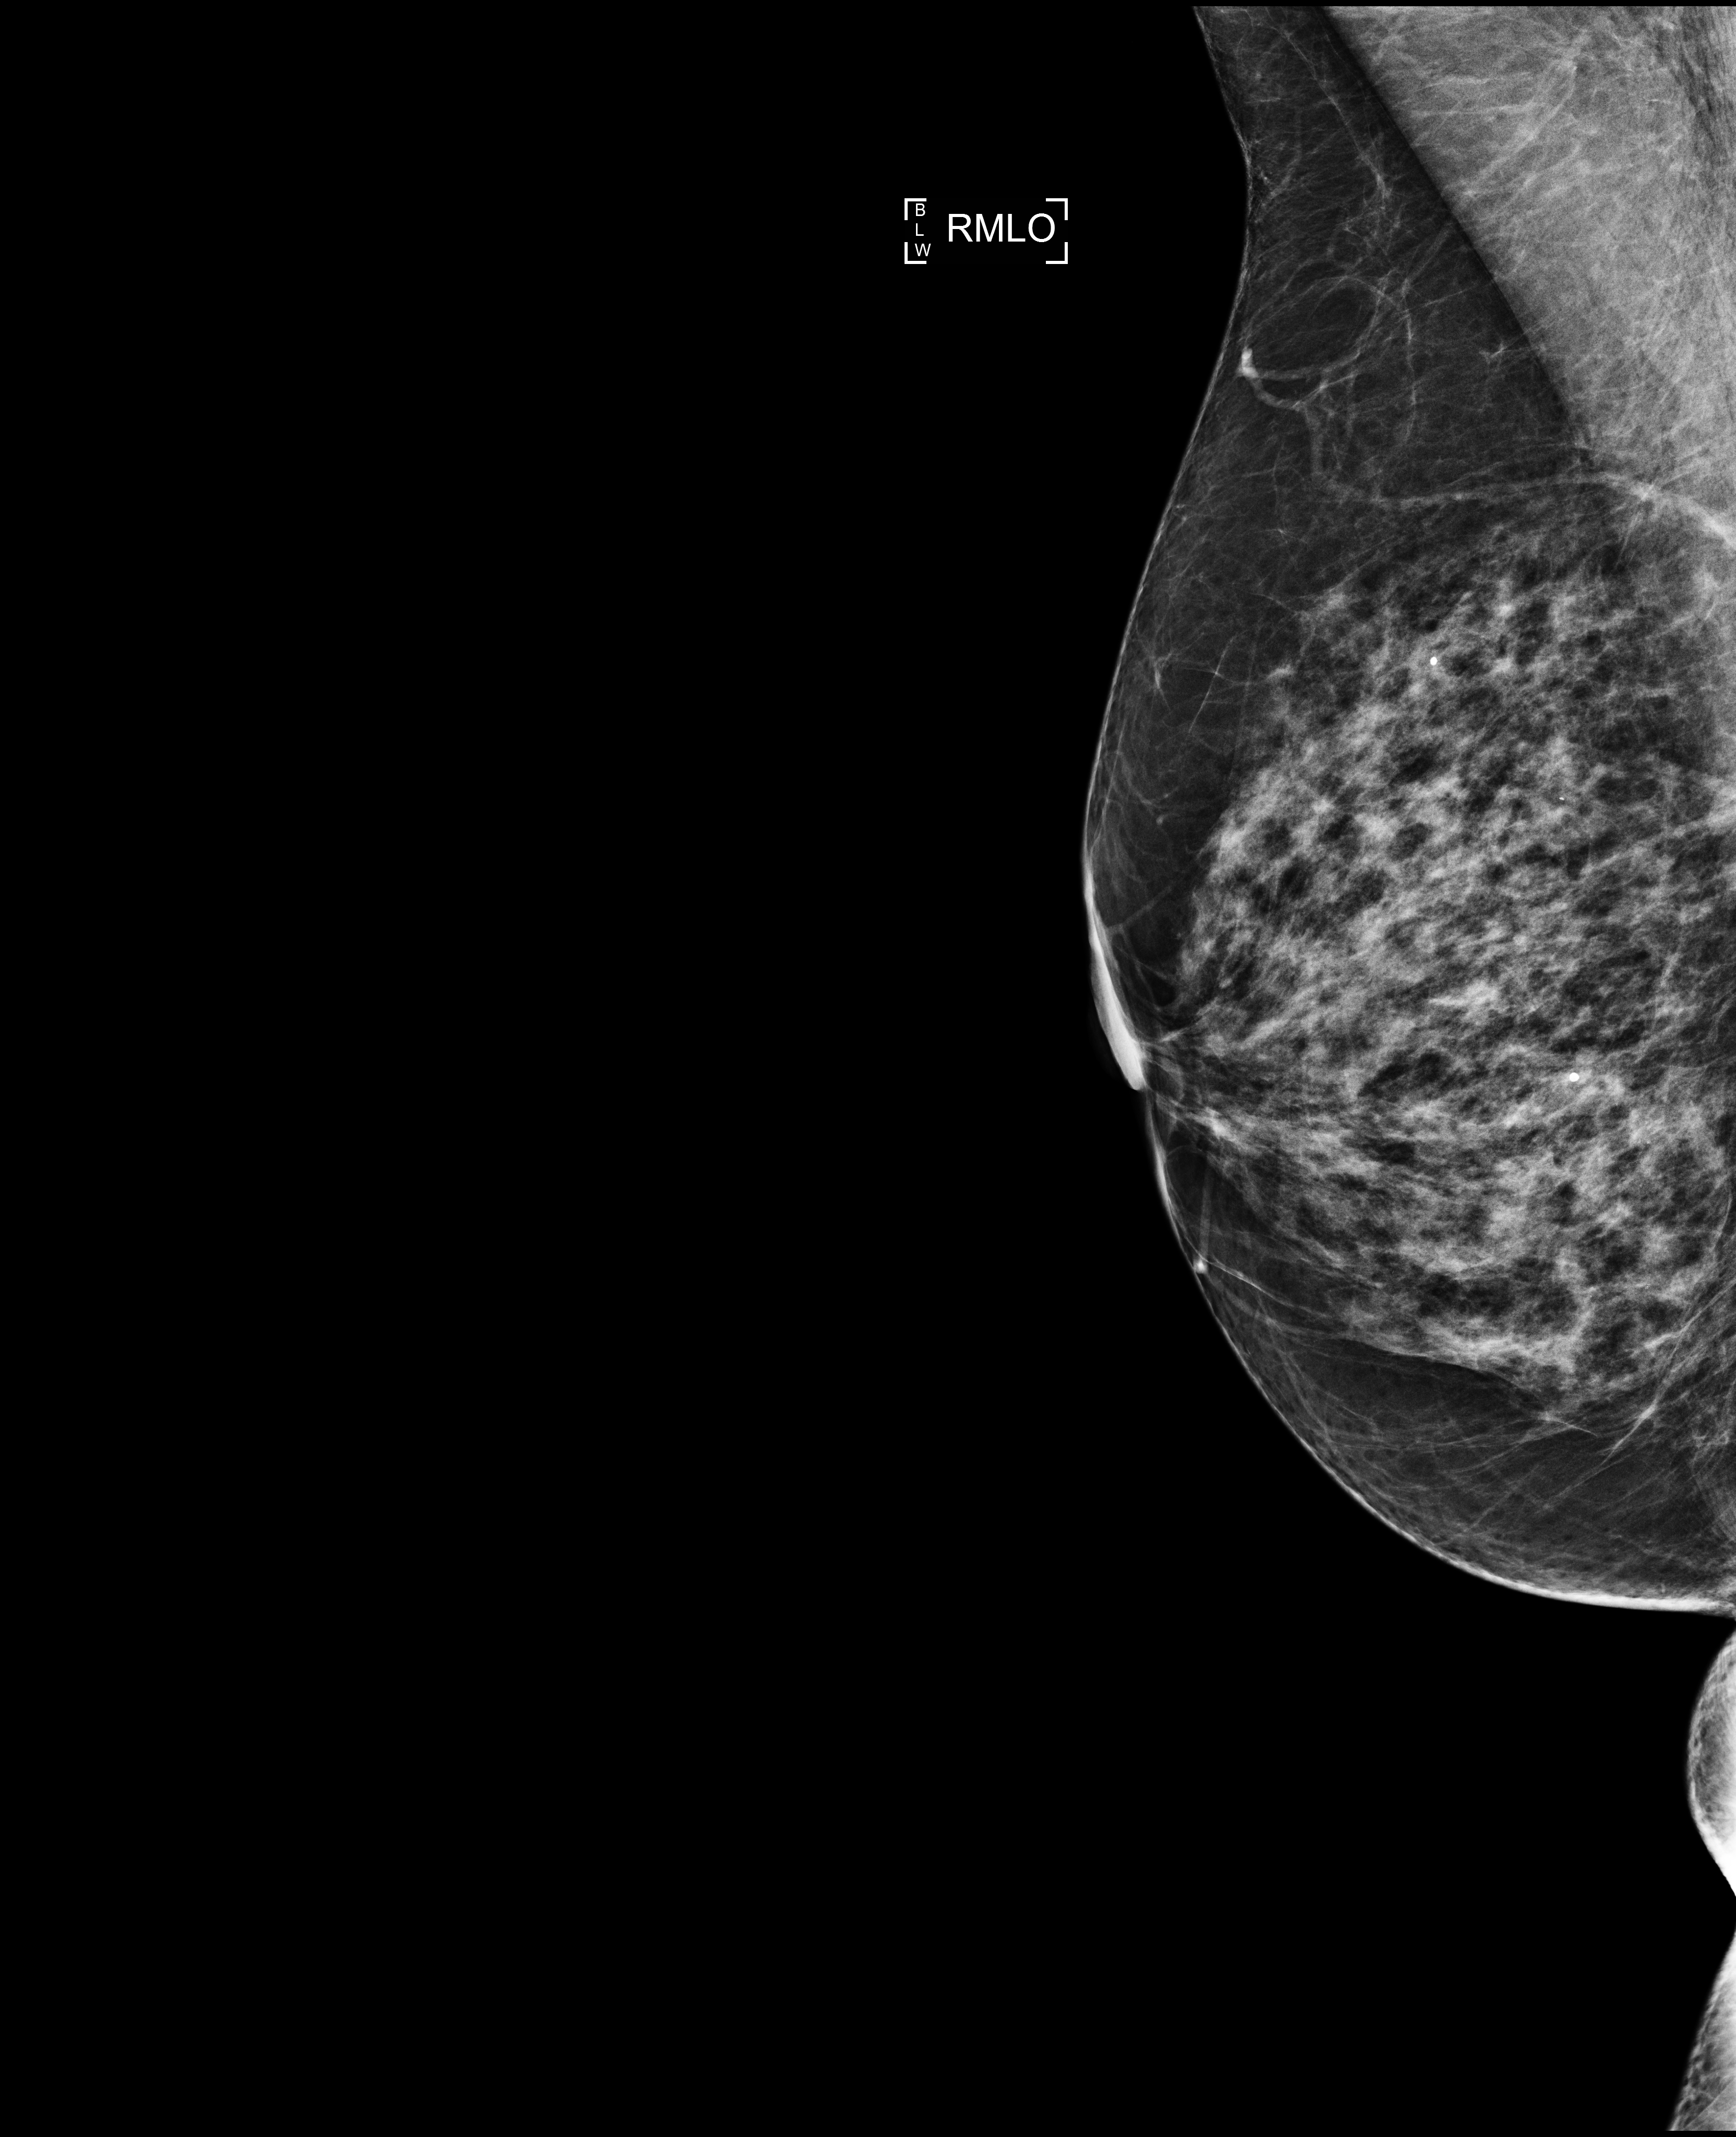
Digital mammogram (FFDM), right breast, mediolateral oblique (MLO) view, annual screening mammography examination, compressed breast thickness 57 mm, system: Selenia Dimensions. Female patient, age 60 years.
BI-RADS breast density category at the screening exam (both breasts, scale 1–4): 3. Final BI-RADS category for the screening round (tomosynthesis exam, both breasts): category 2. Recall: no recall after this screen.